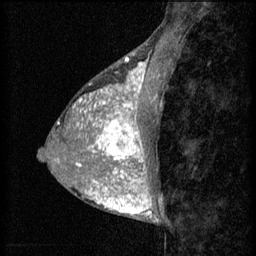
Breast MRI (dynamic contrast-enhanced), one sagittal slice; slice 26 of 60 in the series (ordered by position); 3 images stored at this slice position (order not interpretable as contrast timing); 1.5 T; TE 4.2 ms, TR 8.2 ms; 2 mm slice thickness; 256 × 256 image matrix, field of view 180 × 180 mm. Patient: female, 38 years.
Structures marked on this image (semi-automatic segmentation, software-assisted and operator-edited):
- analysis volume of interest (the breast-tissue region the enhancement analysis was run in; not a lesion): bounding box [x1, y1, x2, y2] px = [95, 106, 156, 171]
- tumour enhancement mask (voxels above the 70 % enhancement threshold inside the analysis volume of interest): [95, 106, 146, 171]